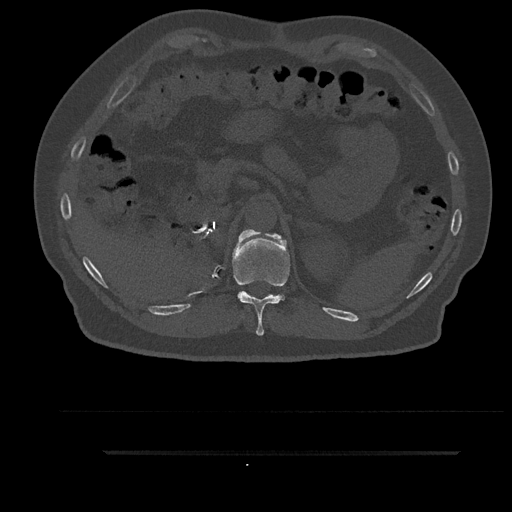
CT including the spine, one axial slice; slice 293 of 797 in the series (ordered by position); reconstruction kernel Br40s/3; 120 kVp; bone window (W 1800 / L 400 HU); 0.5 mm slice thickness; 512 × 512 image matrix, field of view 432 × 432 mm. Patient: male, 63 years. From the clinical record (not read from this slice): primary cancer: renal; vertebrae with lytic lesions (as recorded): T8.
Annotated regions visible in this slice (semi-automatically segmented with operator editing):
- T11 vertebra: box from (x=232, y=229) to (x=290, y=336) px
- T12 vertebra: (x=238, y=231)–(x=256, y=241)